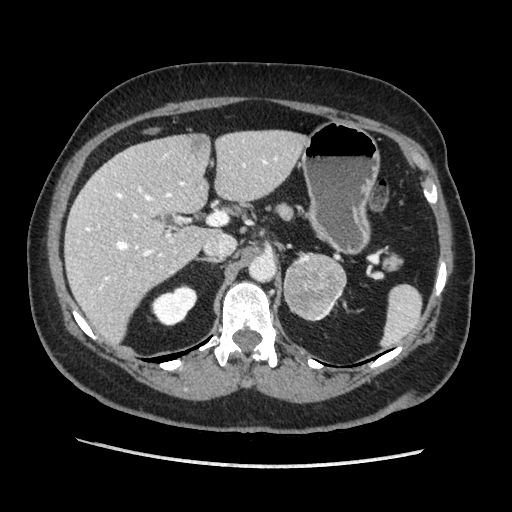
Contrast-enhanced abdominal CT, one axial slice; slice 124 of 203 in the series (ordered by position); soft-tissue window (W 400 / L 40 HU); 1.25 mm slice thickness; 512 × 512 image matrix. Female patient. From the clinical record (not read from this slice): diagnosis: adrenocortical carcinoma; tumour side: left adrenal; tumour size at pathology: 6.5 cm; Ki-67 index: 22 %; stage (as recorded): 2.
Annotated regions visible in this slice (semi-automatic segmentation, software-assisted and operator-edited):
- mass: bounding box <284,252,348,321> (left, top, right, bottom; pixels)